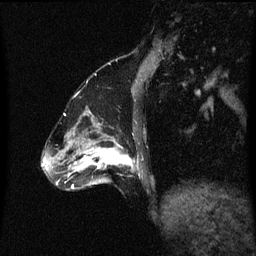
Breast MRI (dynamic contrast-enhanced), one sagittal slice; slice 19 of 60 in the series (ordered by position); dynamic contrast-enhanced series, image 2 of 3 at this slice position (ordered by acquisition); 1.5 T; TE 4.2 ms, TR 8.4 ms; 2 mm slice thickness; 256 × 256 image matrix, field of view 200 × 200 mm. Patient: female, 47 years.
Annotated regions visible in this slice (semi-automatic segmentation, software-assisted and operator-edited):
- analysis volume of interest (the breast-tissue region the enhancement analysis was run in; not a lesion): bounding box <85,136,142,187> (left, top, right, bottom; pixels)
- tumour enhancement mask (voxels above the 70 % enhancement threshold inside the analysis volume of interest): <85,140,134,169>